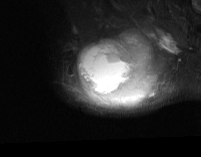
MRI of an extremity soft-tissue mass, one axial slice; position 54 of 74 along the scan axis; STIR; MR volume resampled by the dataset authors to the PET/CT grid (not the native acquisition matrix); 3.27 mm slice thickness; 201 × 157 image matrix, field of view 196 × 153 mm. Male patient. From the clinical record (not read from this slice): histological type: pleiomorphic spindle cell undifferentiated; grade: high; site of the primary tumour: right parascapusular.
Annotated regions visible in this slice (expert contour drawn on MRI and transferred to this co-registered scan by the dataset authors):
- gross tumour volume including surrounding oedema: bounding box <72,34,178,108> (left, top, right, bottom; pixels)
- gross tumour volume (mass): <78,39,152,106>